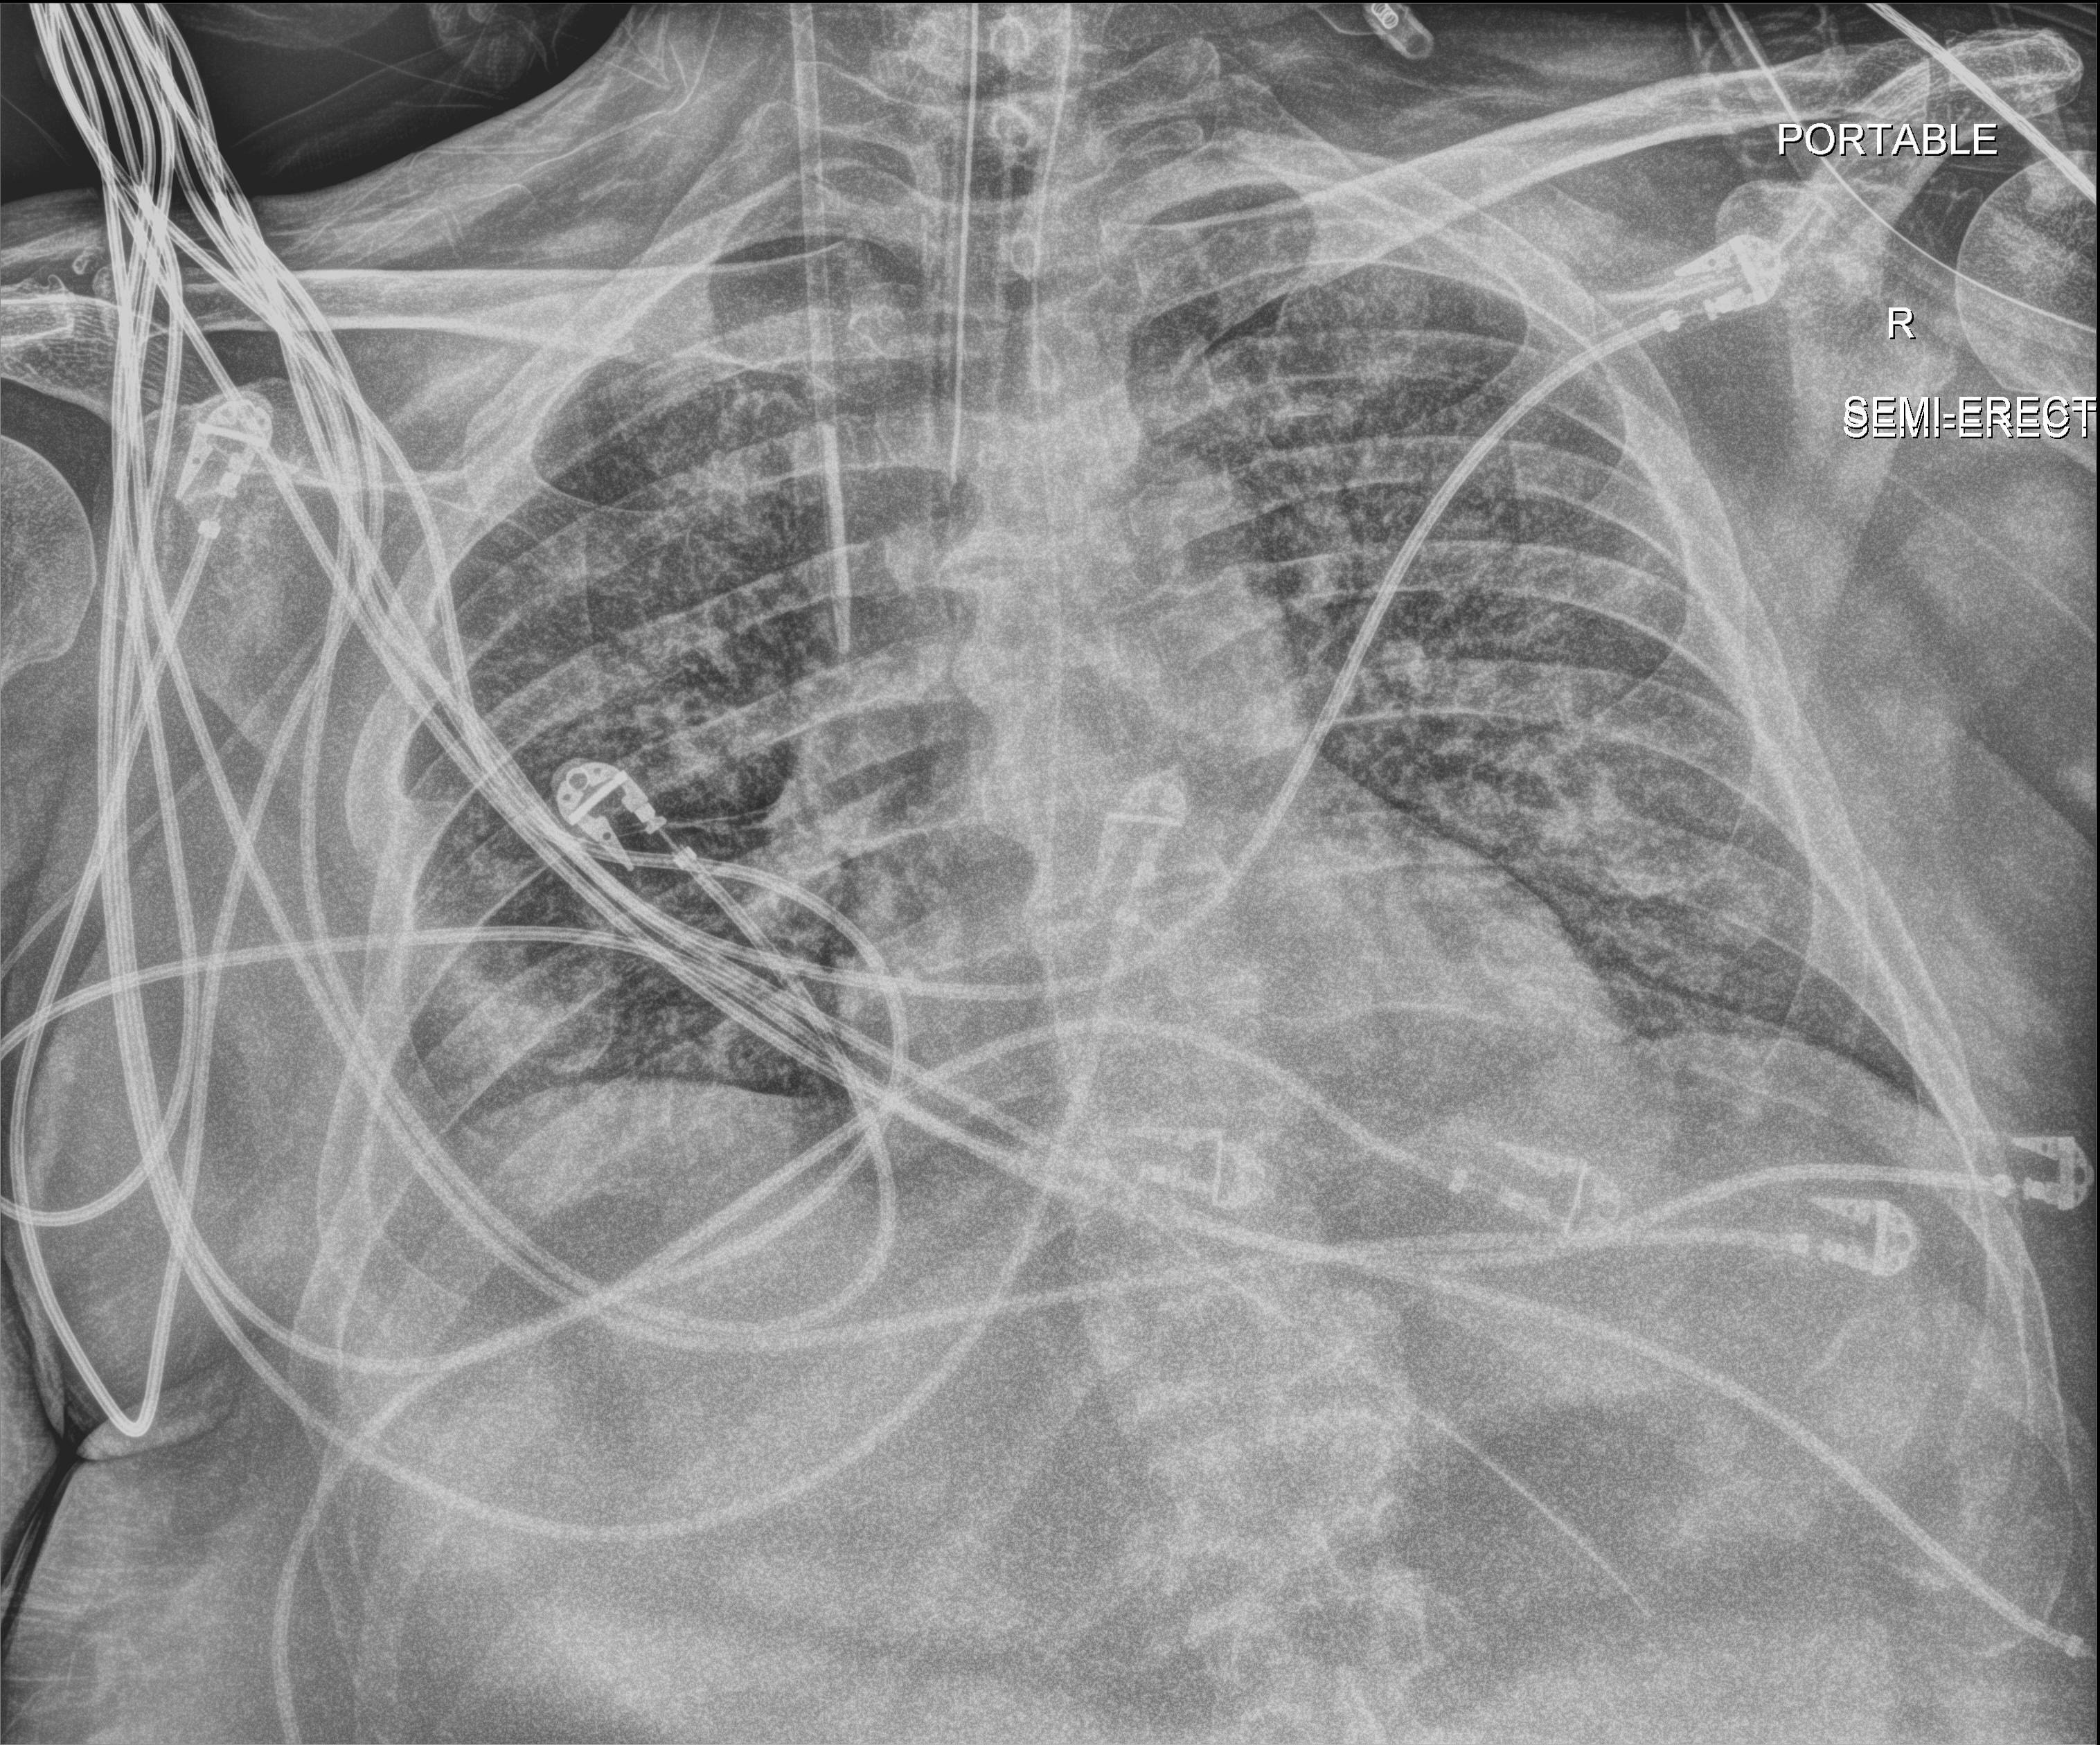
Portable chest radiograph; anteroposterior (AP) projection. Male patient hospitalised with COVID-19, age 60–74 years.
From the hospital-stay record, not from the radiograph (when in the stay this image was taken is not recorded): diabetes (admission record): yes; mechanically ventilated during this hospital stay: yes.